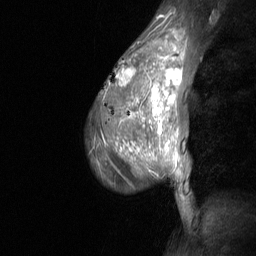
Breast MRI (dynamic contrast-enhanced), one sagittal slice; slice 46 of 64 in the series (ordered by position); dynamic contrast-enhanced study with each time point stored as its own series, time point 2 of 3 at this slice position (early post-contrast, ordered by acquisition time); 1.5 T; TE 4.8 ms, TR 27 ms; 256 × 256 image matrix. Patient: female, 36 years. From the clinical record (not read from this slice): setting: breast cancer imaged before/during neoadjuvant chemotherapy; receptor status: HR-positive, HER2-negative.
Annotated regions visible in this slice (semi-automatic segmentation, software-assisted and operator-edited):
- analysis volume of interest (the breast-tissue region the enhancement analysis was run in; not a lesion): bounding box <88,45,187,210> (left, top, right, bottom; pixels)
- tumour enhancement mask (voxels above the 90 % enhancement threshold inside the analysis volume of interest): <116,46,183,147>